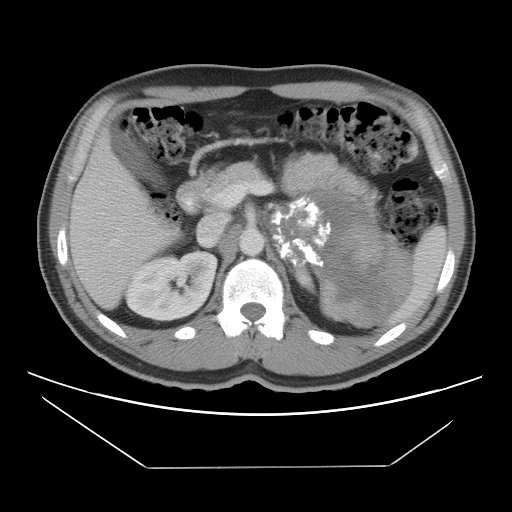
Contrast-enhanced abdominal CT, one axial slice; position 69 of 131 along the scan axis; intravenous contrast given; soft-tissue window (W 400 / L 40 HU); 5 mm slice thickness; 512 × 512 image matrix, field of view 396 × 396 mm. Patient: male, 44 years. Case-level facts recorded for this patient, not image findings: diagnosis: adrenocortical carcinoma; tumour side: left adrenal; tumour size at pathology: 15.5 cm; Ki-67 index: 6 %; stage (as recorded): 2.
Outlined on this slice (semi-automatically segmented with operator editing):
- mass: box from (x=269, y=190) to (x=408, y=324) px